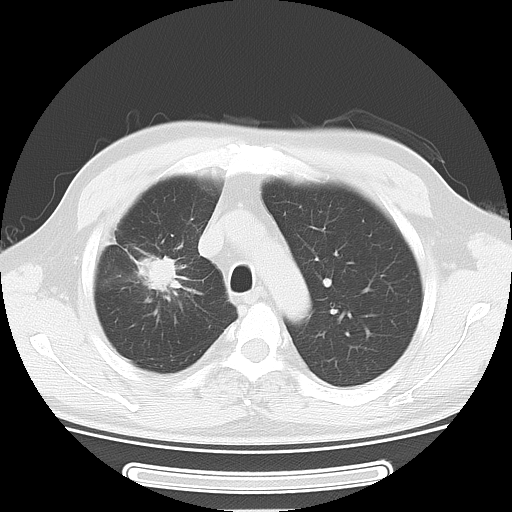
Chest CT, one axial slice. Slice 40 of 51 in the series (ordered by position). Reconstruction kernel LUNG. Lung window (W 1500 / L -600 HU). 5 mm slice thickness. 512 × 512 image matrix, field of view 350 × 350 mm. Patient: male, 46 years. From the clinical record (not read from this slice): clinical TNM (as recorded): T3 N0 M1b.
Structures marked on this image (bounding box drawn by a radiologist):
- lung tumour (recorded histology: adenocarcinoma): bounding box <131,242,189,307> (left, top, right, bottom; pixels)